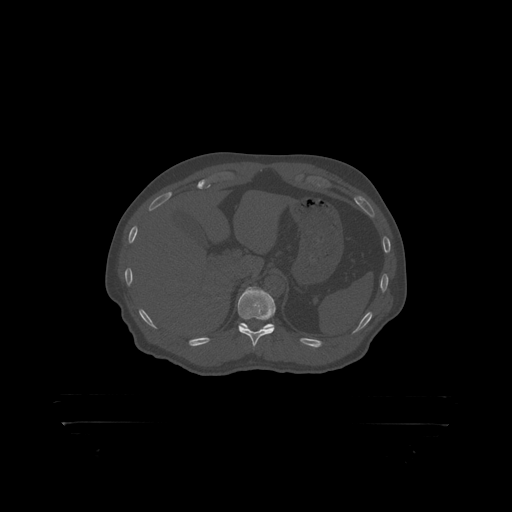
CT including the spine, one axial slice. Position 372 of 399 along the scan axis. Reconstruction kernel STANDARD. Bone window (W 1800 / L 400 HU). 1.25 mm slice thickness. 512 × 512 image matrix, field of view 650 × 650 mm. Male patient, age 46 years. Case-level facts recorded for this patient, not image findings: primary cancer: skin.
Outlined on this slice (semi-automatic segmentation, software-assisted and operator-edited):
- T11 vertebra: bounding box [x1, y1, x2, y2] px = [238, 288, 276, 319]